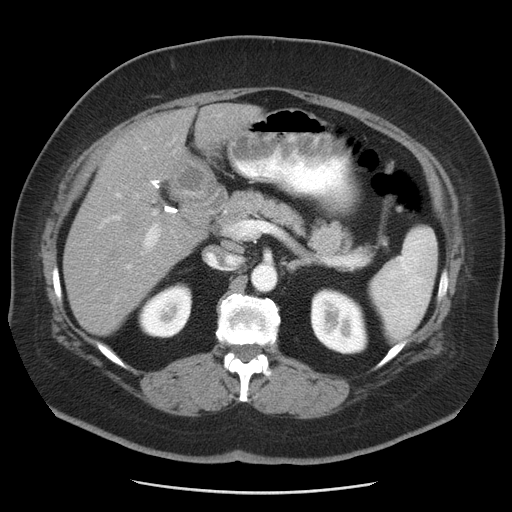
Contrast-enhanced abdominal CT, one axial slice. Reconstruction kernel STANDARD. 120 kVp. Intravenous contrast given. Soft-tissue window (W 400 / L 40 HU). 5 mm slice thickness. 512 × 512 image matrix, field of view 380 × 380 mm. Female patient, age 52 years. From the clinical record (not read from this slice): diagnosis: colorectal cancer liver metastases, imaged before liver resection; multiple liver metastases: yes; largest metastasis: 2.5 cm; disease in both lobes: yes.
Outlined on this slice (manually delineated by an expert):
- liver: bounding box (x1, y1, x2, y2) in pixels: (63, 104, 260, 336)
- planned liver remnant (the part of the liver to remain after resection): (63, 198, 199, 336)
- portal vein (with intrahepatic branches): (97, 146, 175, 272)